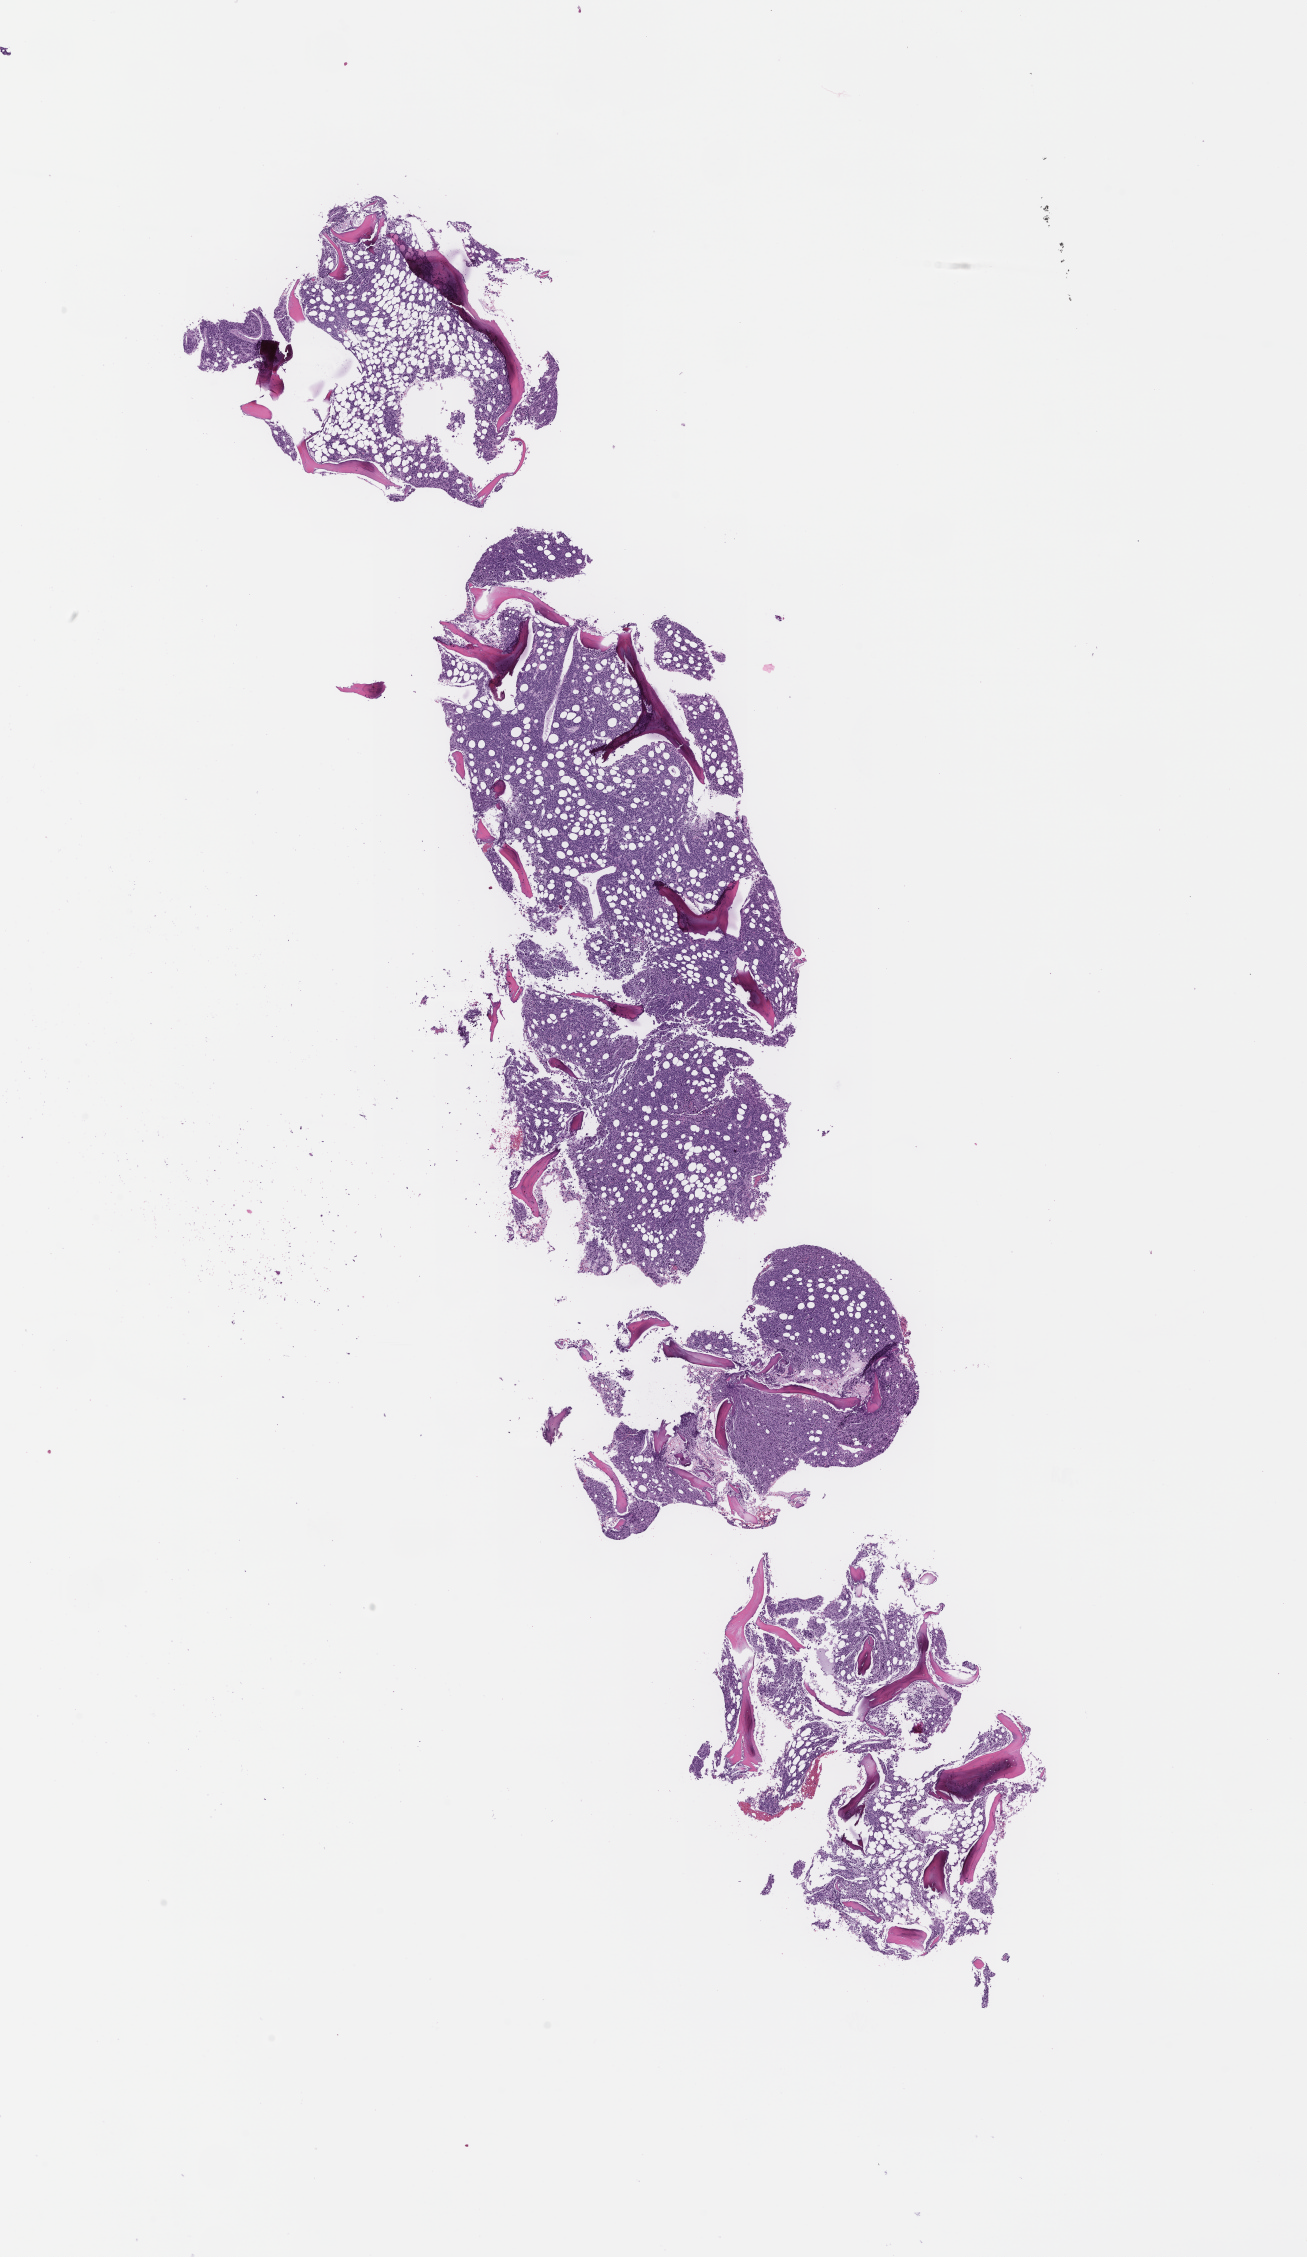
H&E whole-slide image — whole scanned area (about 10.6 x 18.2 mm) shown as a low-resolution overview; FFPE section; site: bone marrow; specimen time point: archival tissue. Patient: female.
* this section: primary tumor
* diagnosis: Plasma Cell Myeloma